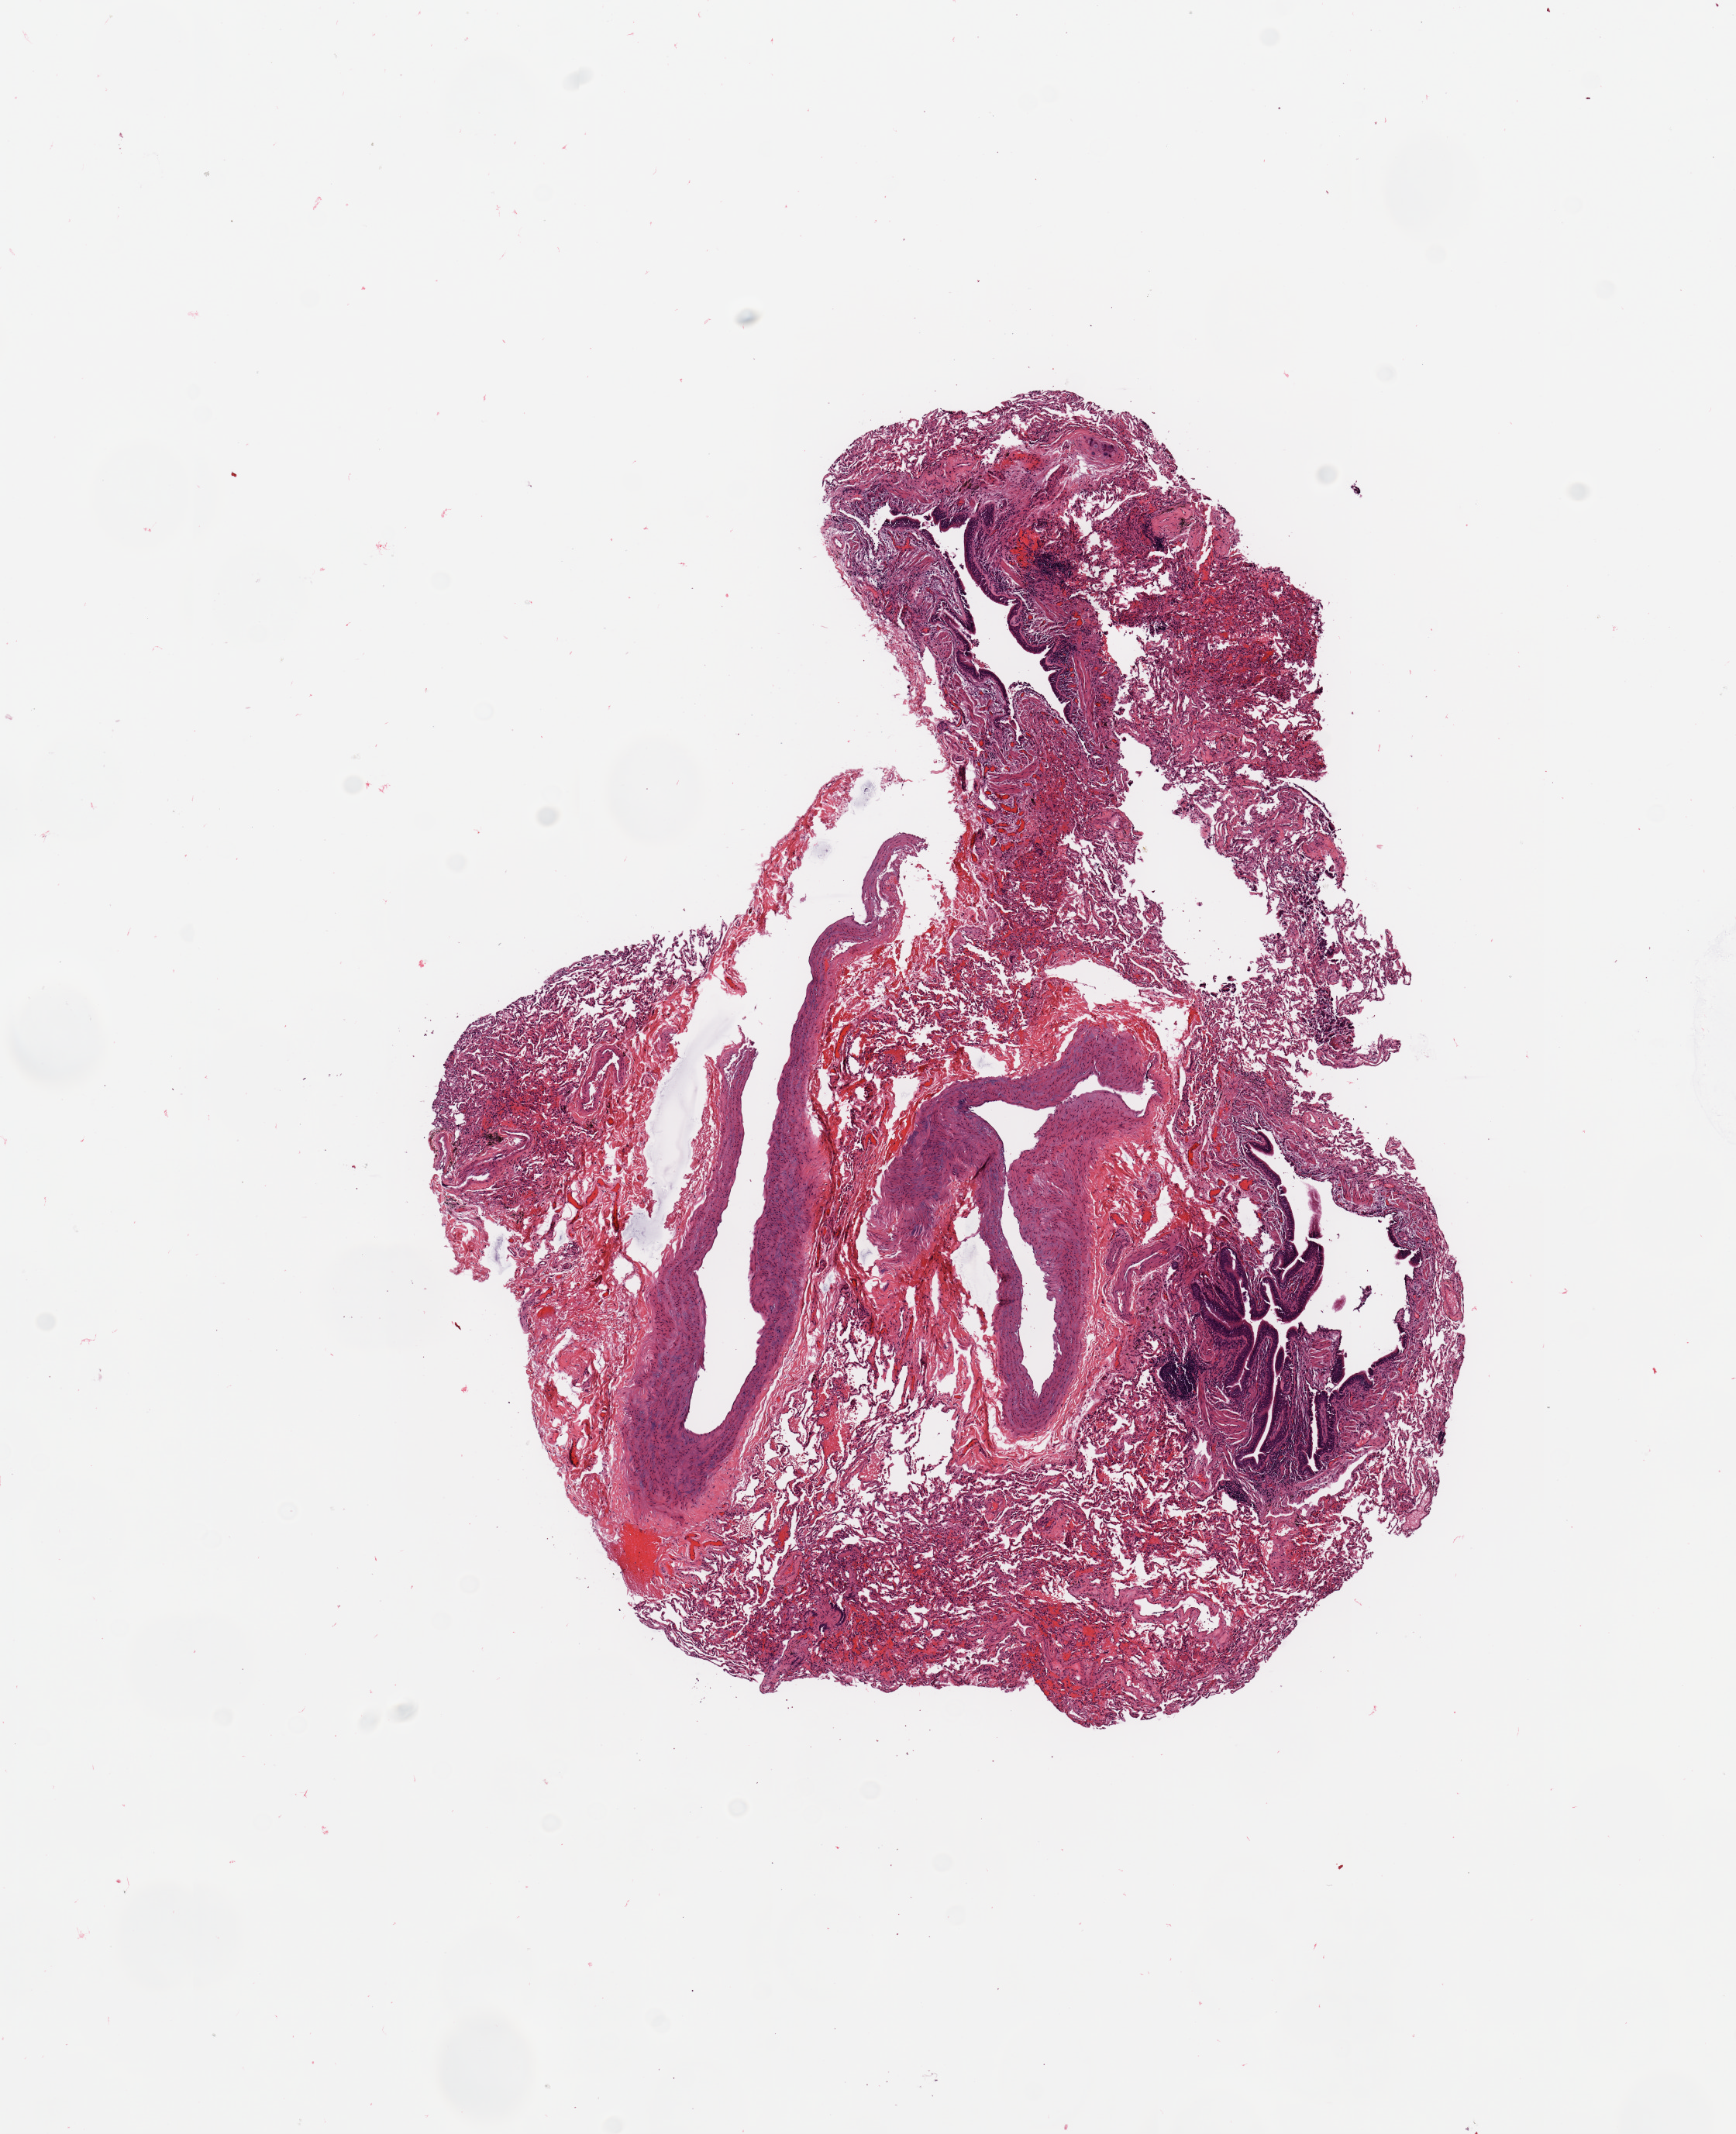
Digitized H&E tissue section (whole slide), shown as a low-resolution overview of the whole scanned area (about 8.9 x 10.9 mm, from a 20x scan); normal (non-tumour) tissue sample, lung. Male, 65 y/o.
This section: normal (non-tumour) tissue from the same patient. Patient diagnosis: Adenocarcinoma, NOS.